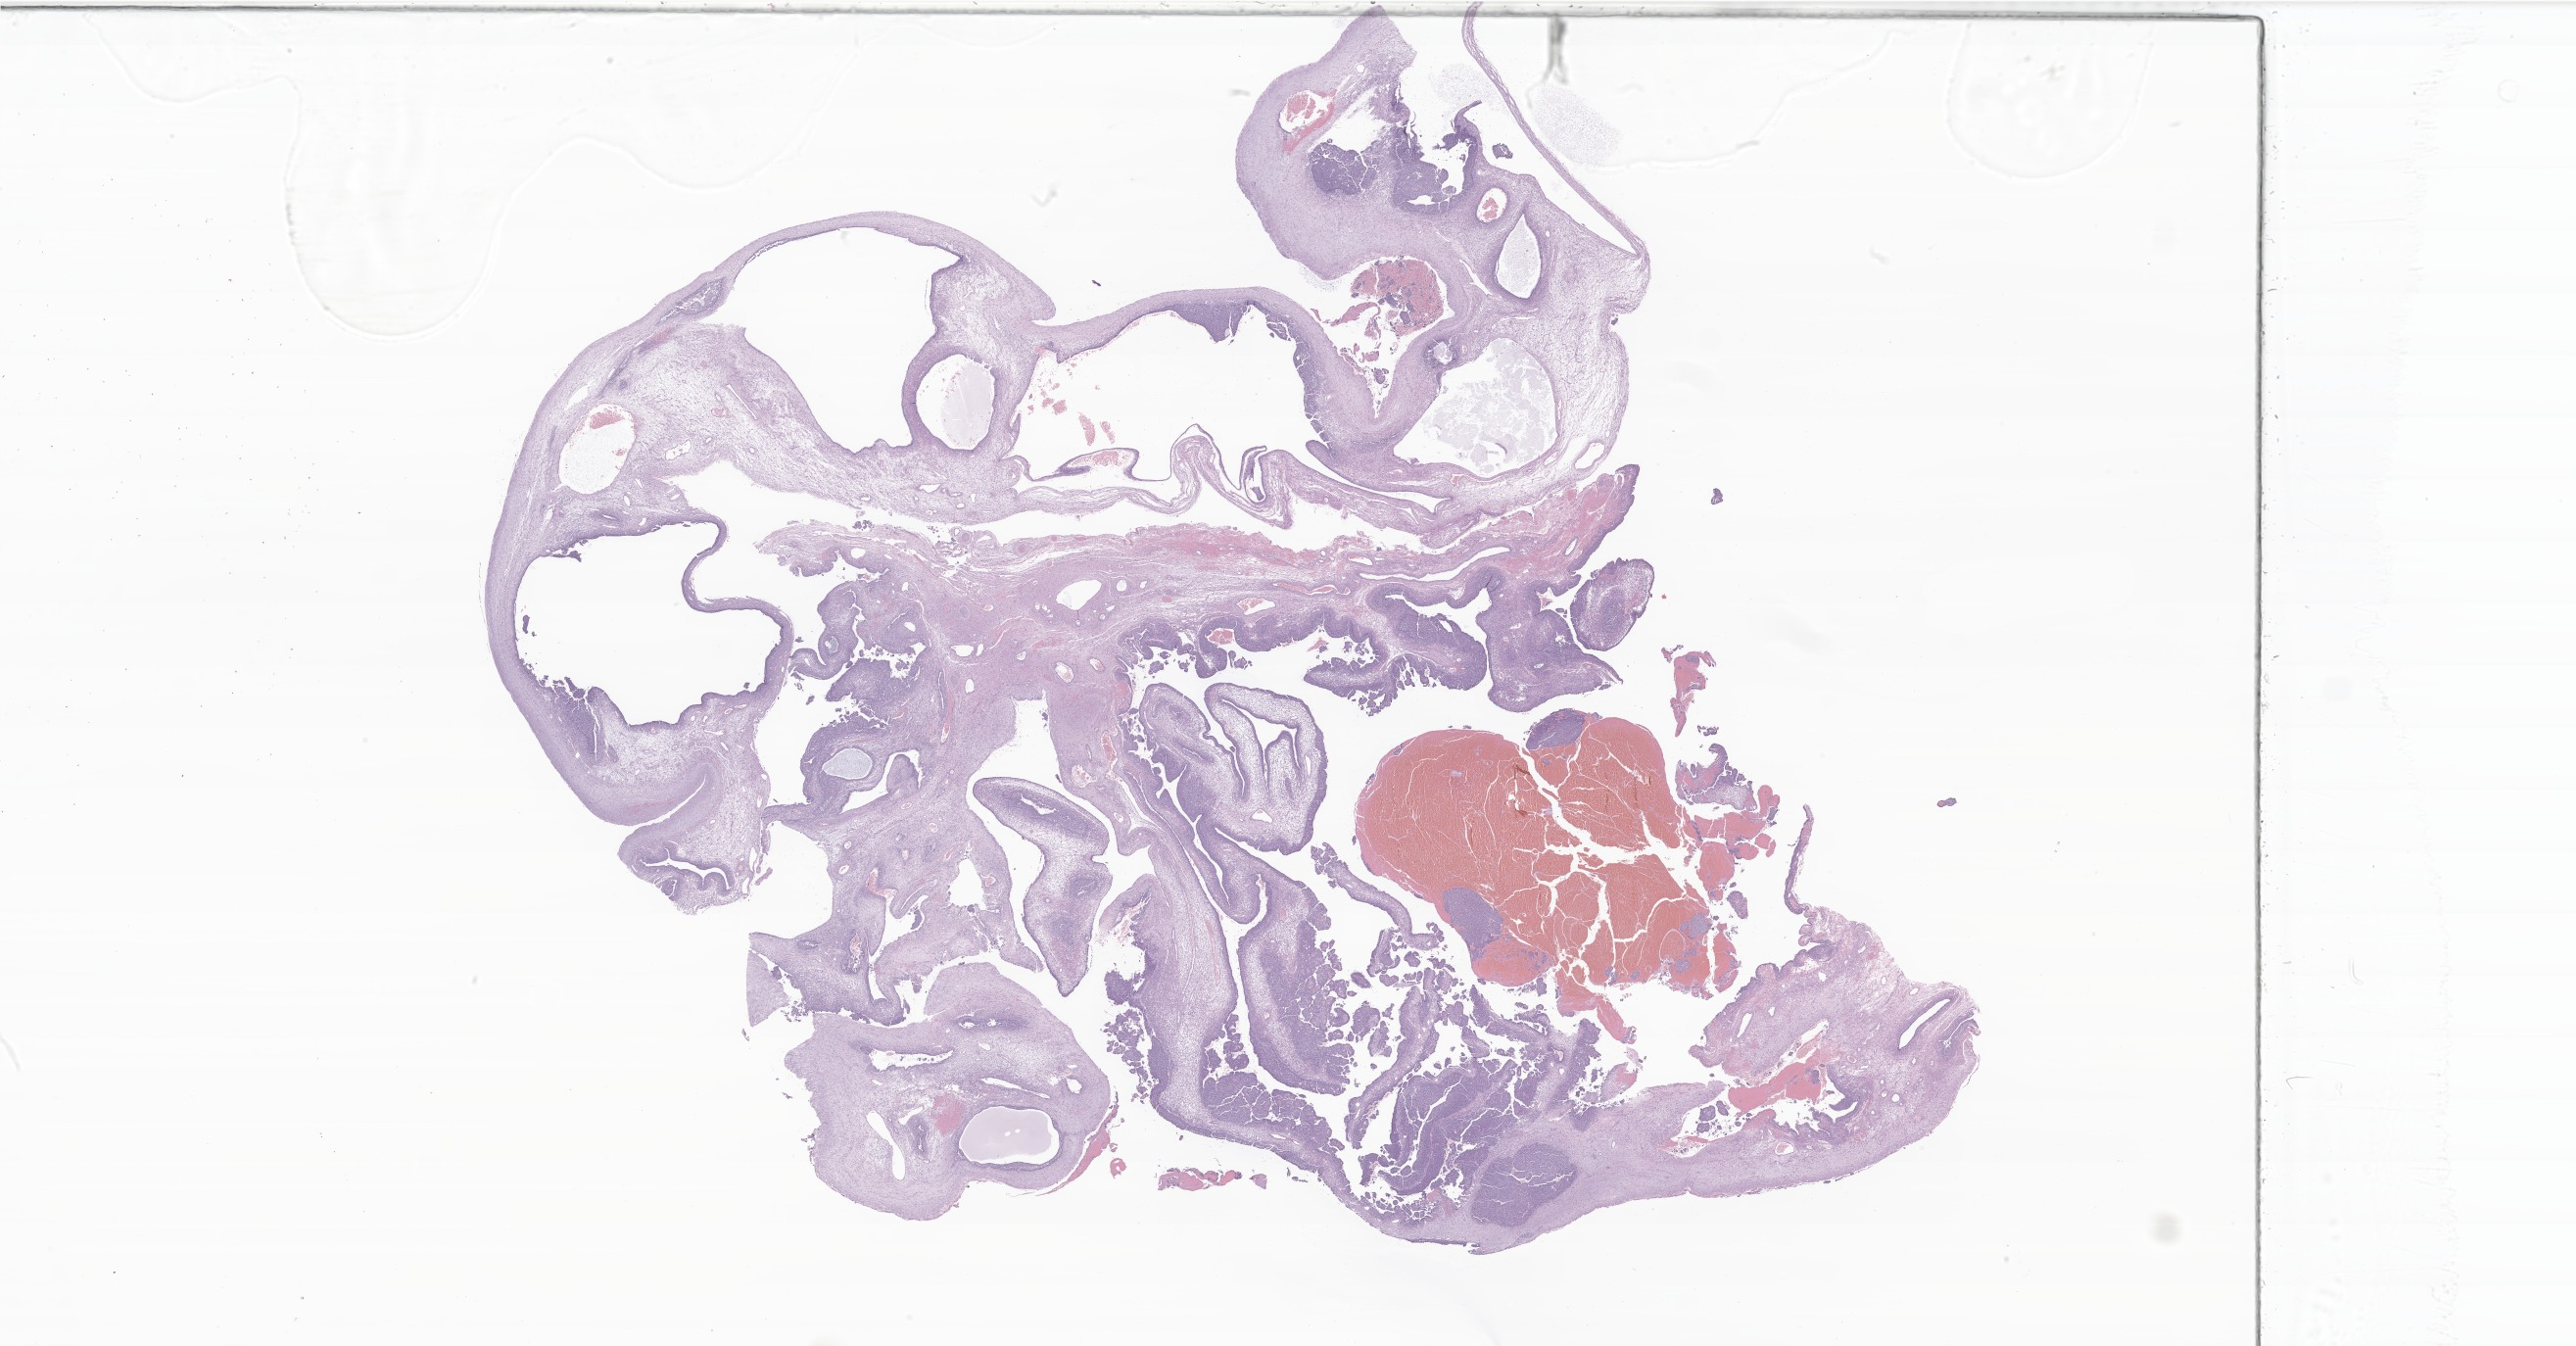
H&E whole-slide image of tumor tissue from the ovary — a low-resolution overview of the entire scanned area, about 44.4 x 23.2 mm. Formalin-fixed, paraffin-embedded (FFPE) tissue. Female patient, age 197 months (16 years 5 months).
Diagnosis: Adult granulosa cell tumor of testis.